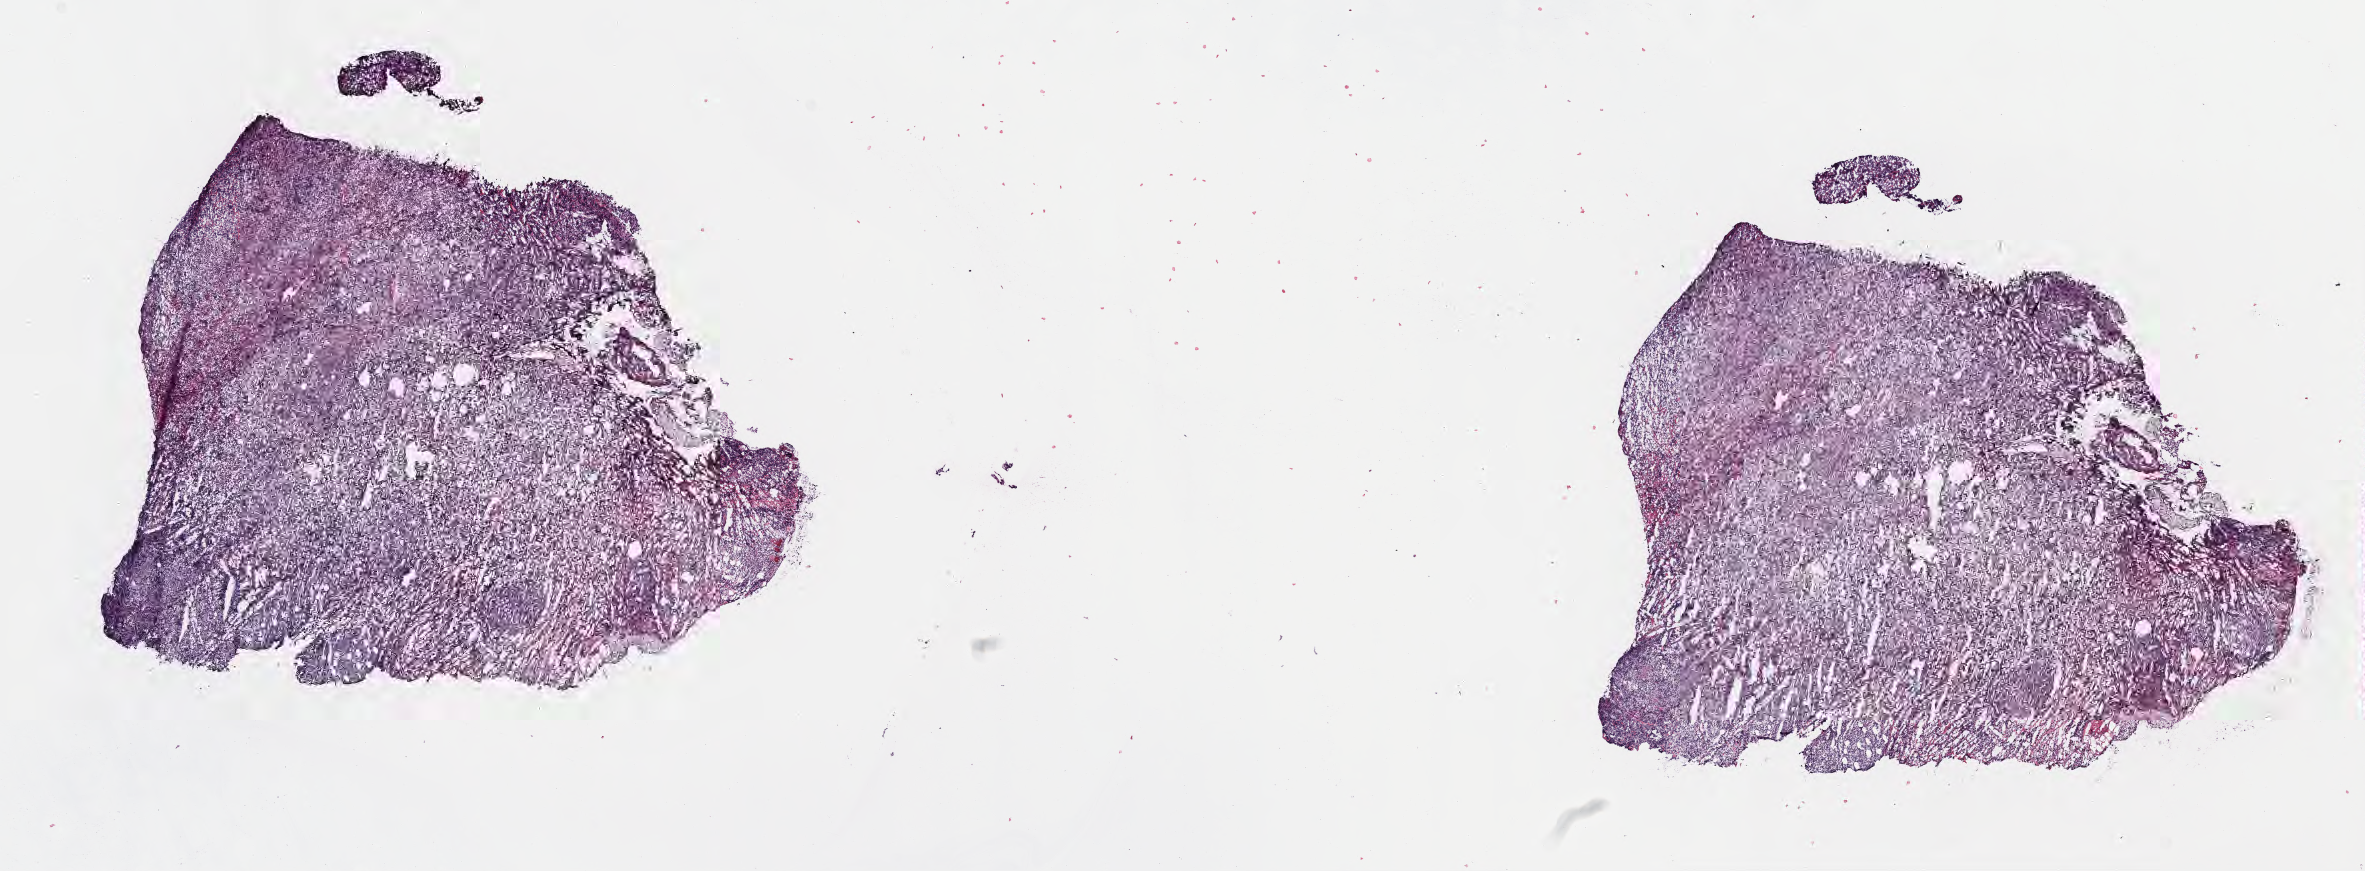
Whole-slide image, H&E stain, low-resolution overview of the scanned area, about 19.1 x 7.0 mm, cryosection, specimen: primary tumor, anatomic site: mandible. Patient: male, age at initial diagnosis 7 years. Composition of this section per pathologist review: tumor cells 90%, tumor nuclei 90%, stromal cells 5%, necrosis 5%, normal cells 0%. Inflammatory infiltration, as recorded: lymphocyte infiltration 50%, monocyte infiltration 20%, neutrophil infiltration 20%.
• Ann Arbor stage (patient): Stage III
• section: top of the tissue portion
• diagnosis: Burkitt lymphoma, NOS